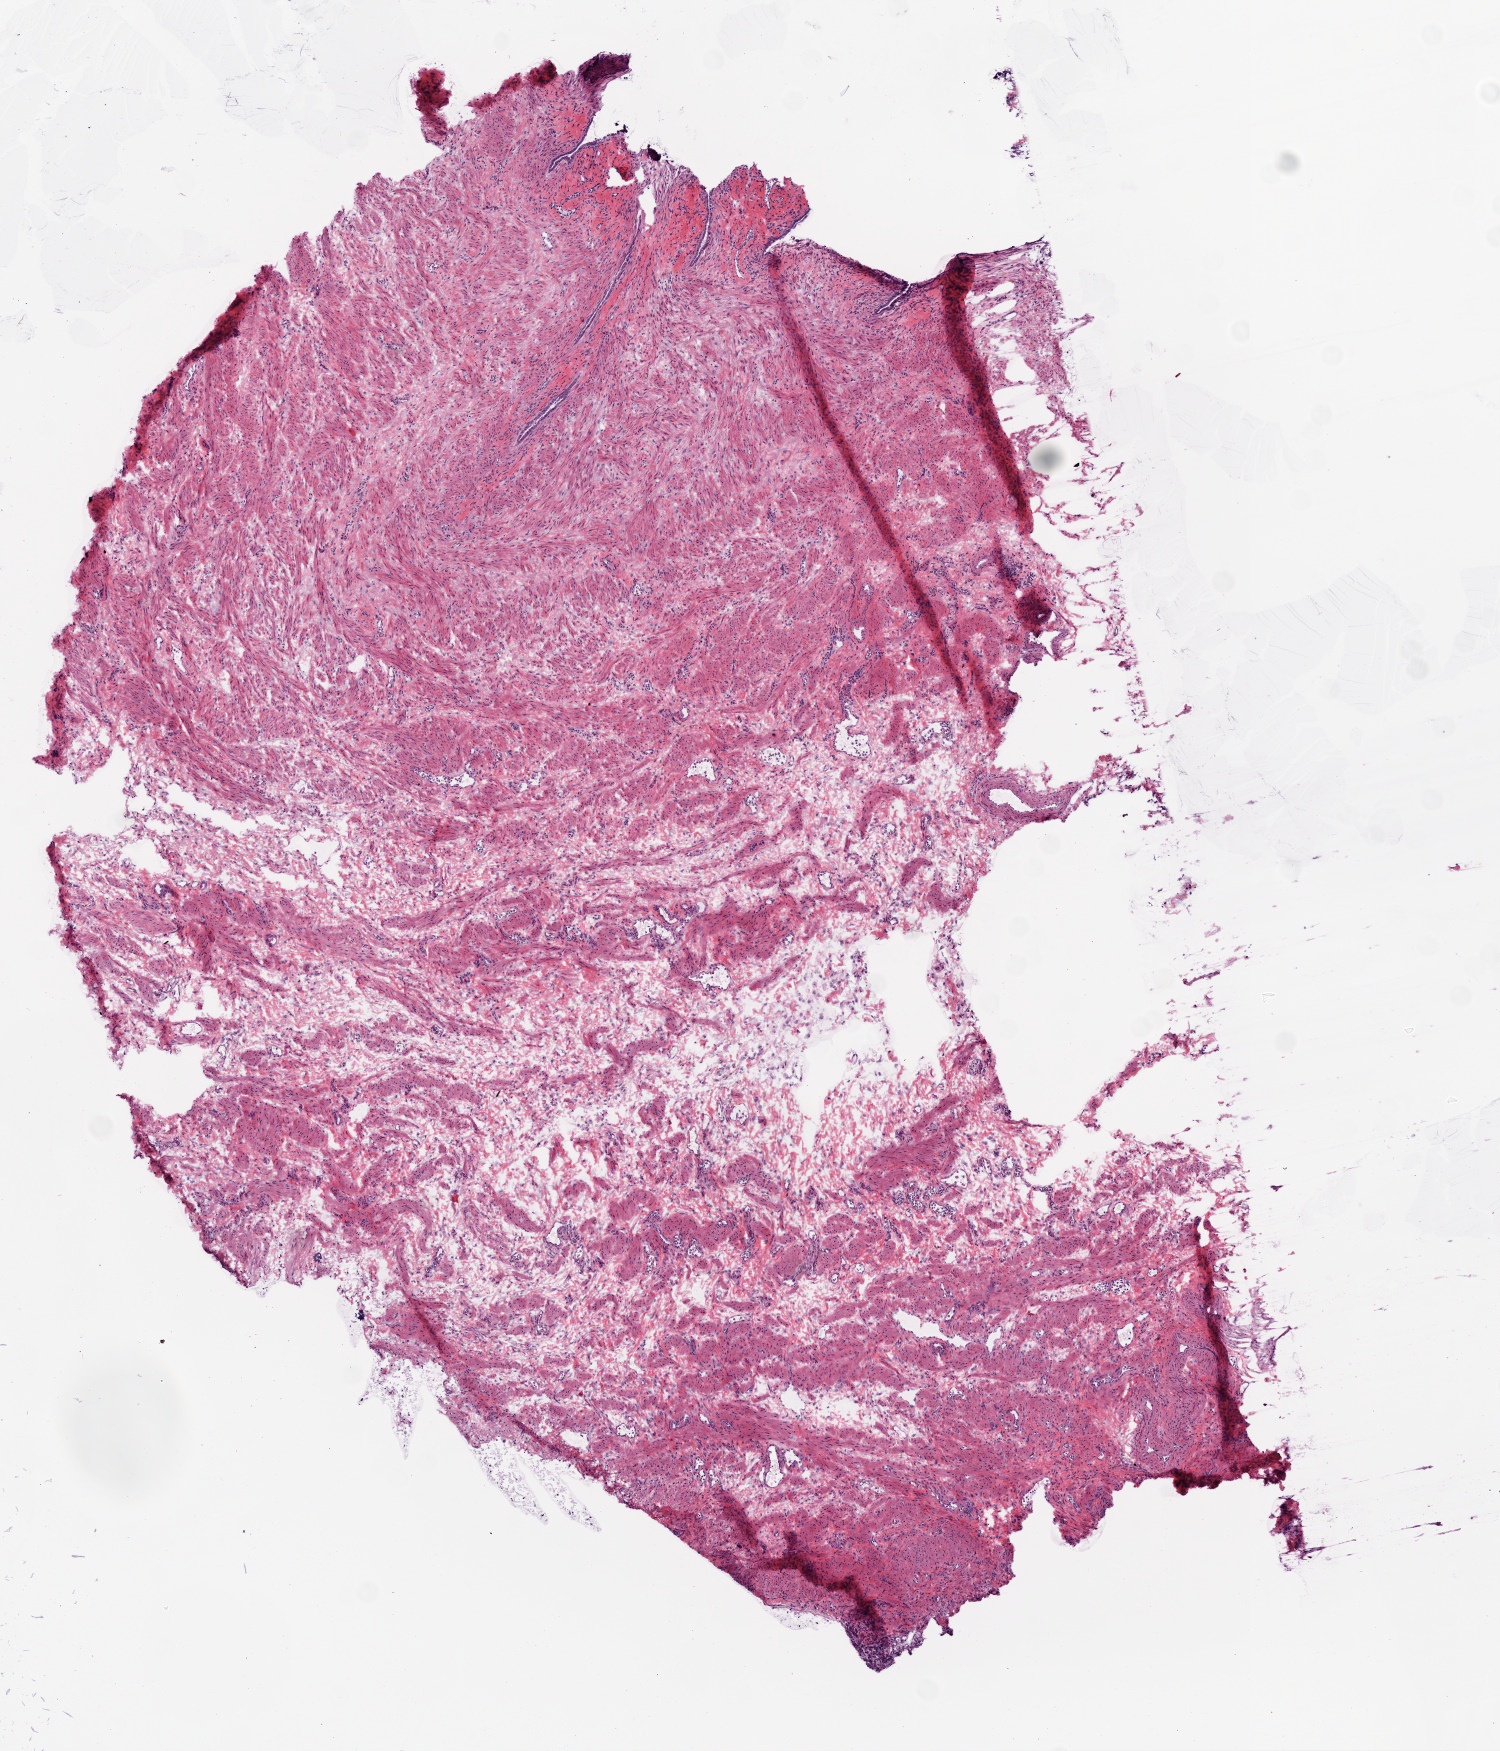
Whole-slide histology image, Hematoxylin and eosin (H&E) stained, whole scanned area (about 6.0 x 7.0 mm) shown as a low-resolution overview. Frozen section. Sample: solid tissue normal (non-tumour tissue), ovary. Female patient; age at initial diagnosis 58 years.
This section: solid tissue normal (non-tumour) sample from the same patient. Patient diagnosis: Serous cystadenocarcinoma, NOS.